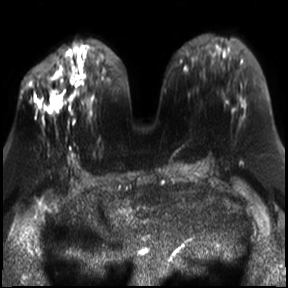
Breast MRI, one axial slice. Slice 13 of 30 in the series (ordered by position). Diffusion-weighted series; image 2 of 4 stored at this slice position (different b-values; order by instance number). 3 T. 4 mm slice thickness. 288 × 288 image matrix. Female patient.
Structures marked on this image (expert manual segmentation):
- tumour on diffusion-weighted imaging: box from (x=50, y=96) to (x=63, y=107) px